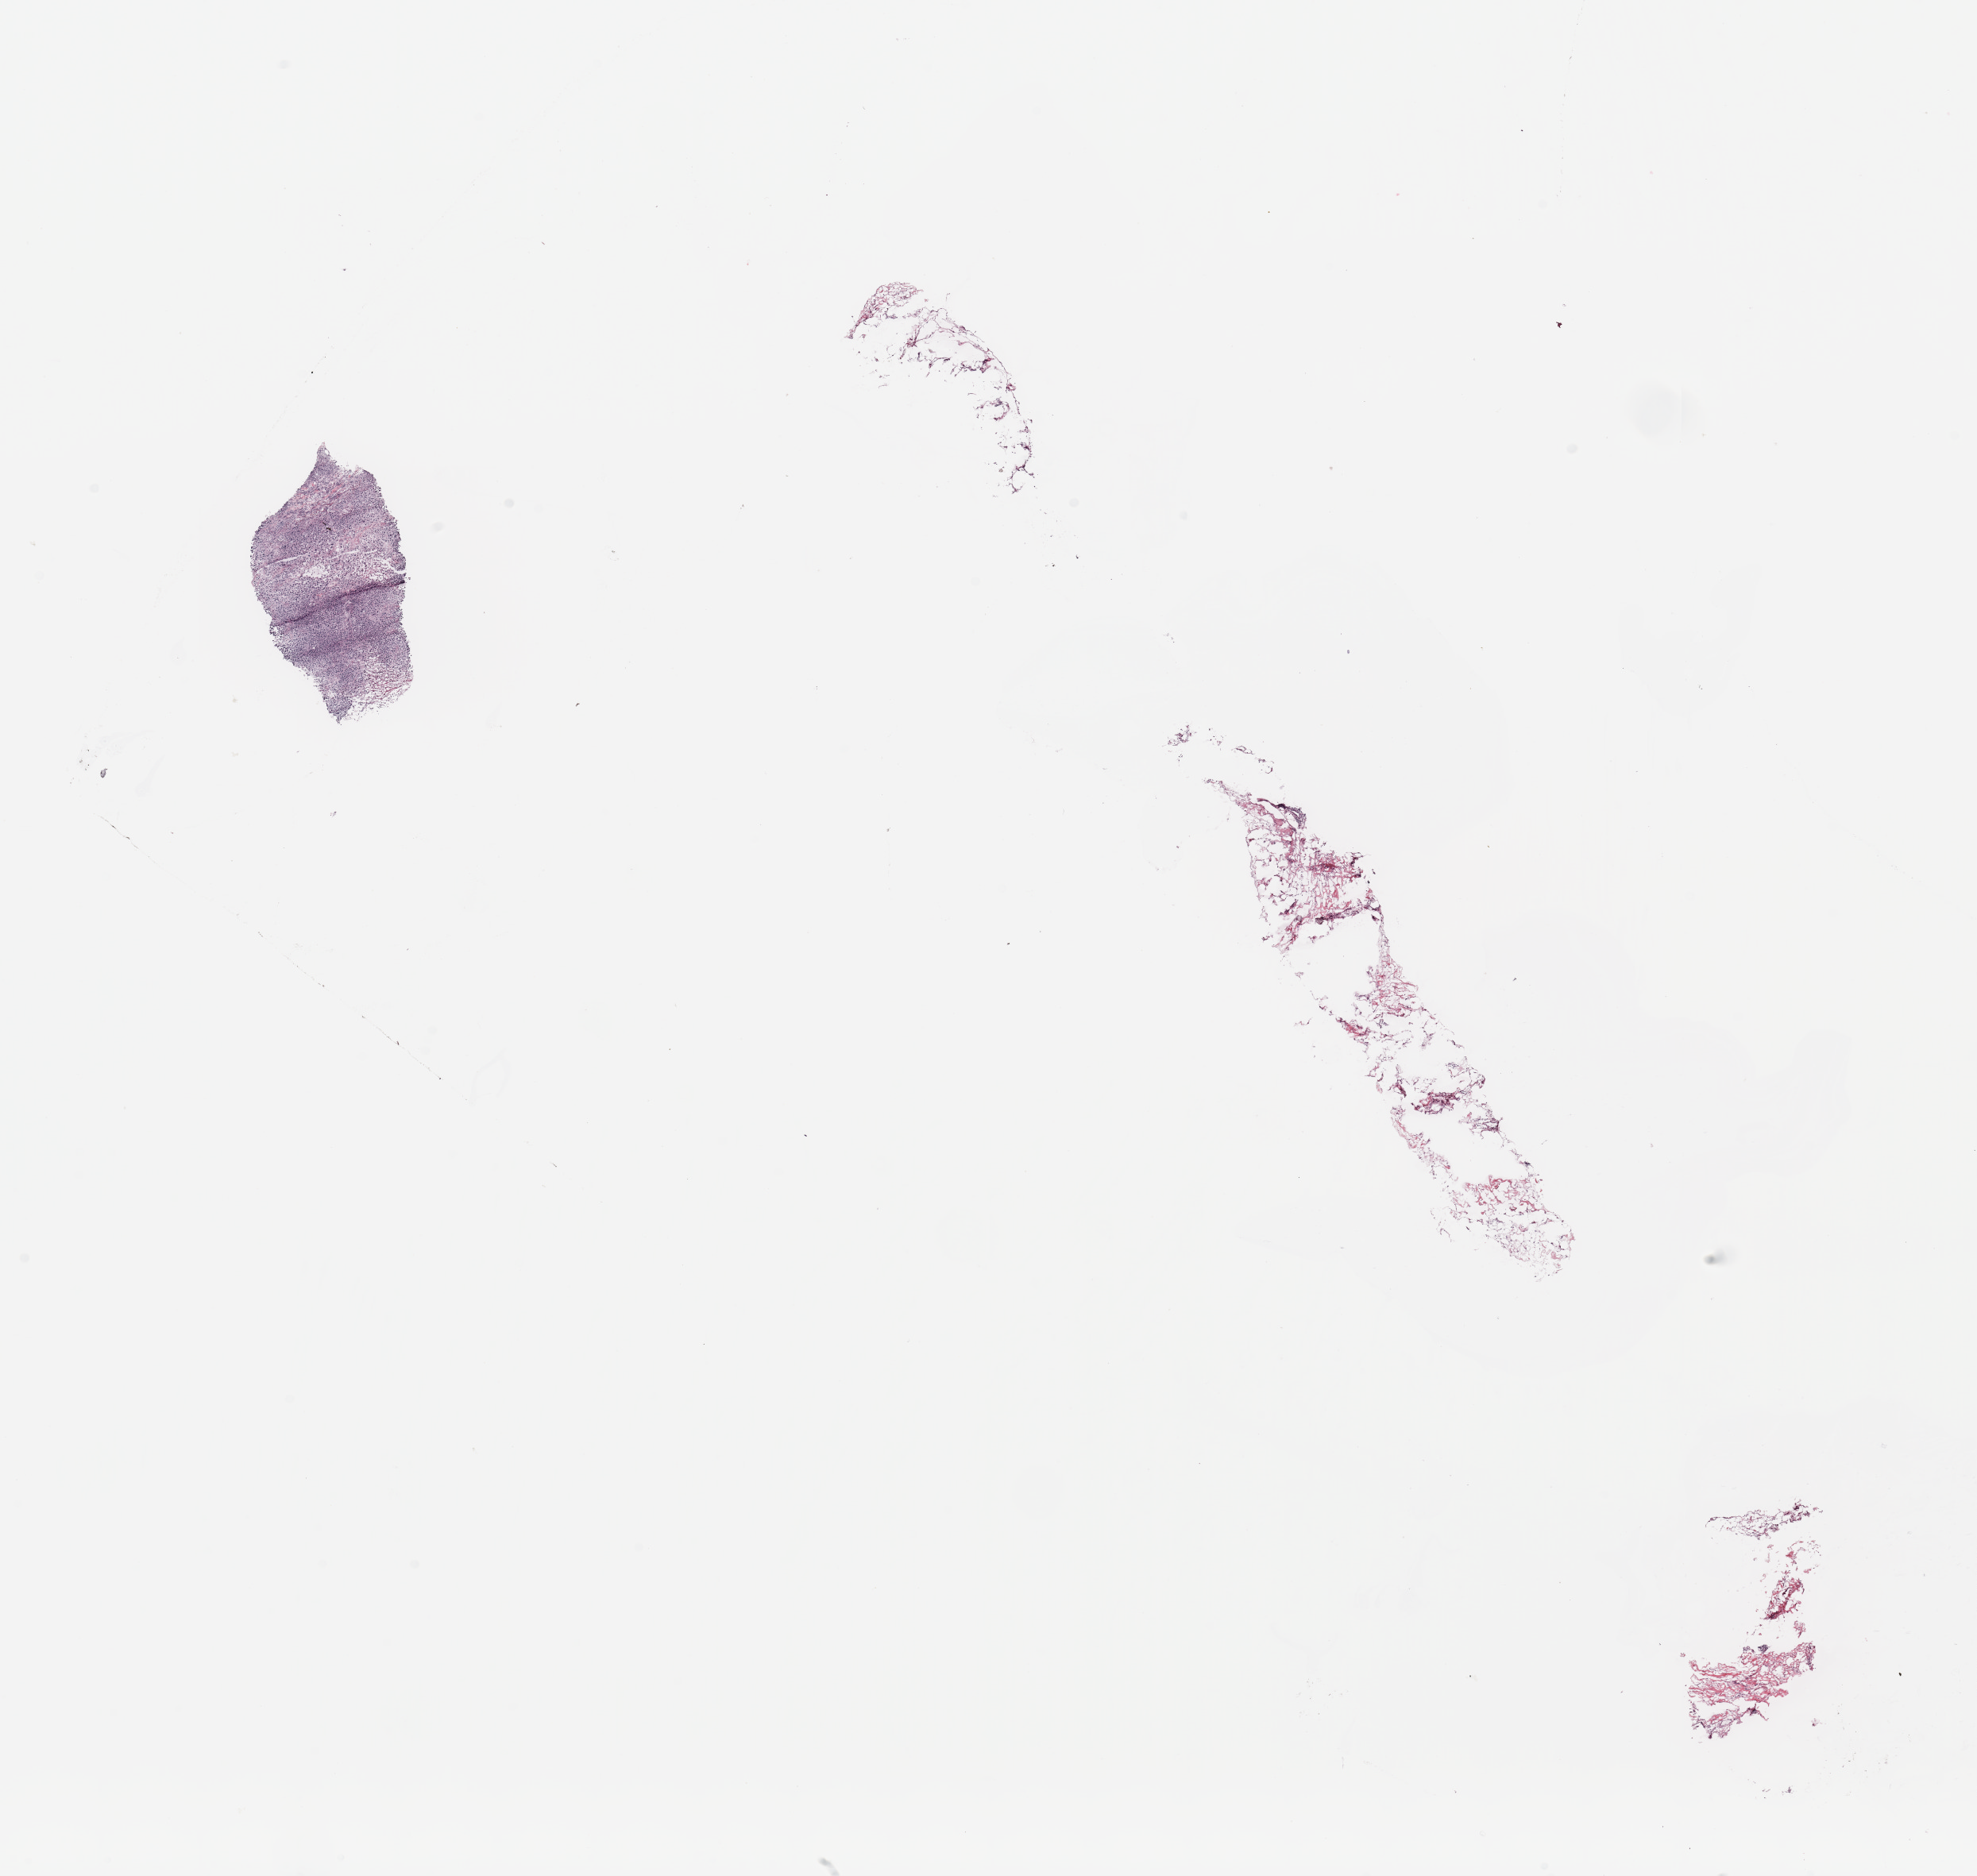
Whole-slide histology image, H&E-stained, whole scanned area (about 19.7 x 18.7 mm, from a 20x scan) shown as a low-resolution overview, breast, tissue type not recorded. 59-year-old female patient.
Patient diagnosis: Adenocarcinoma, NOS.